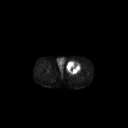
FDG PET of an extremity soft-tissue mass (from a PET/CT study), one axial slice. Slice 257 of 267 in the series (ordered by position). 128 × 128 image matrix, field of view 700 × 700 mm. Patient: male, 63 years. Case-level facts recorded for this patient, not image findings: histological type: pleiomorphic liposarcoma; grade: high; site of the primary tumour: left thigh.
Annotated regions visible in this slice (expert contour drawn on MRI and transferred to this co-registered scan by the dataset authors):
- gross tumour volume including surrounding oedema: bounding box (x1, y1, x2, y2) in pixels: (67, 60, 81, 72)
- gross tumour volume (mass): (67, 61, 80, 72)